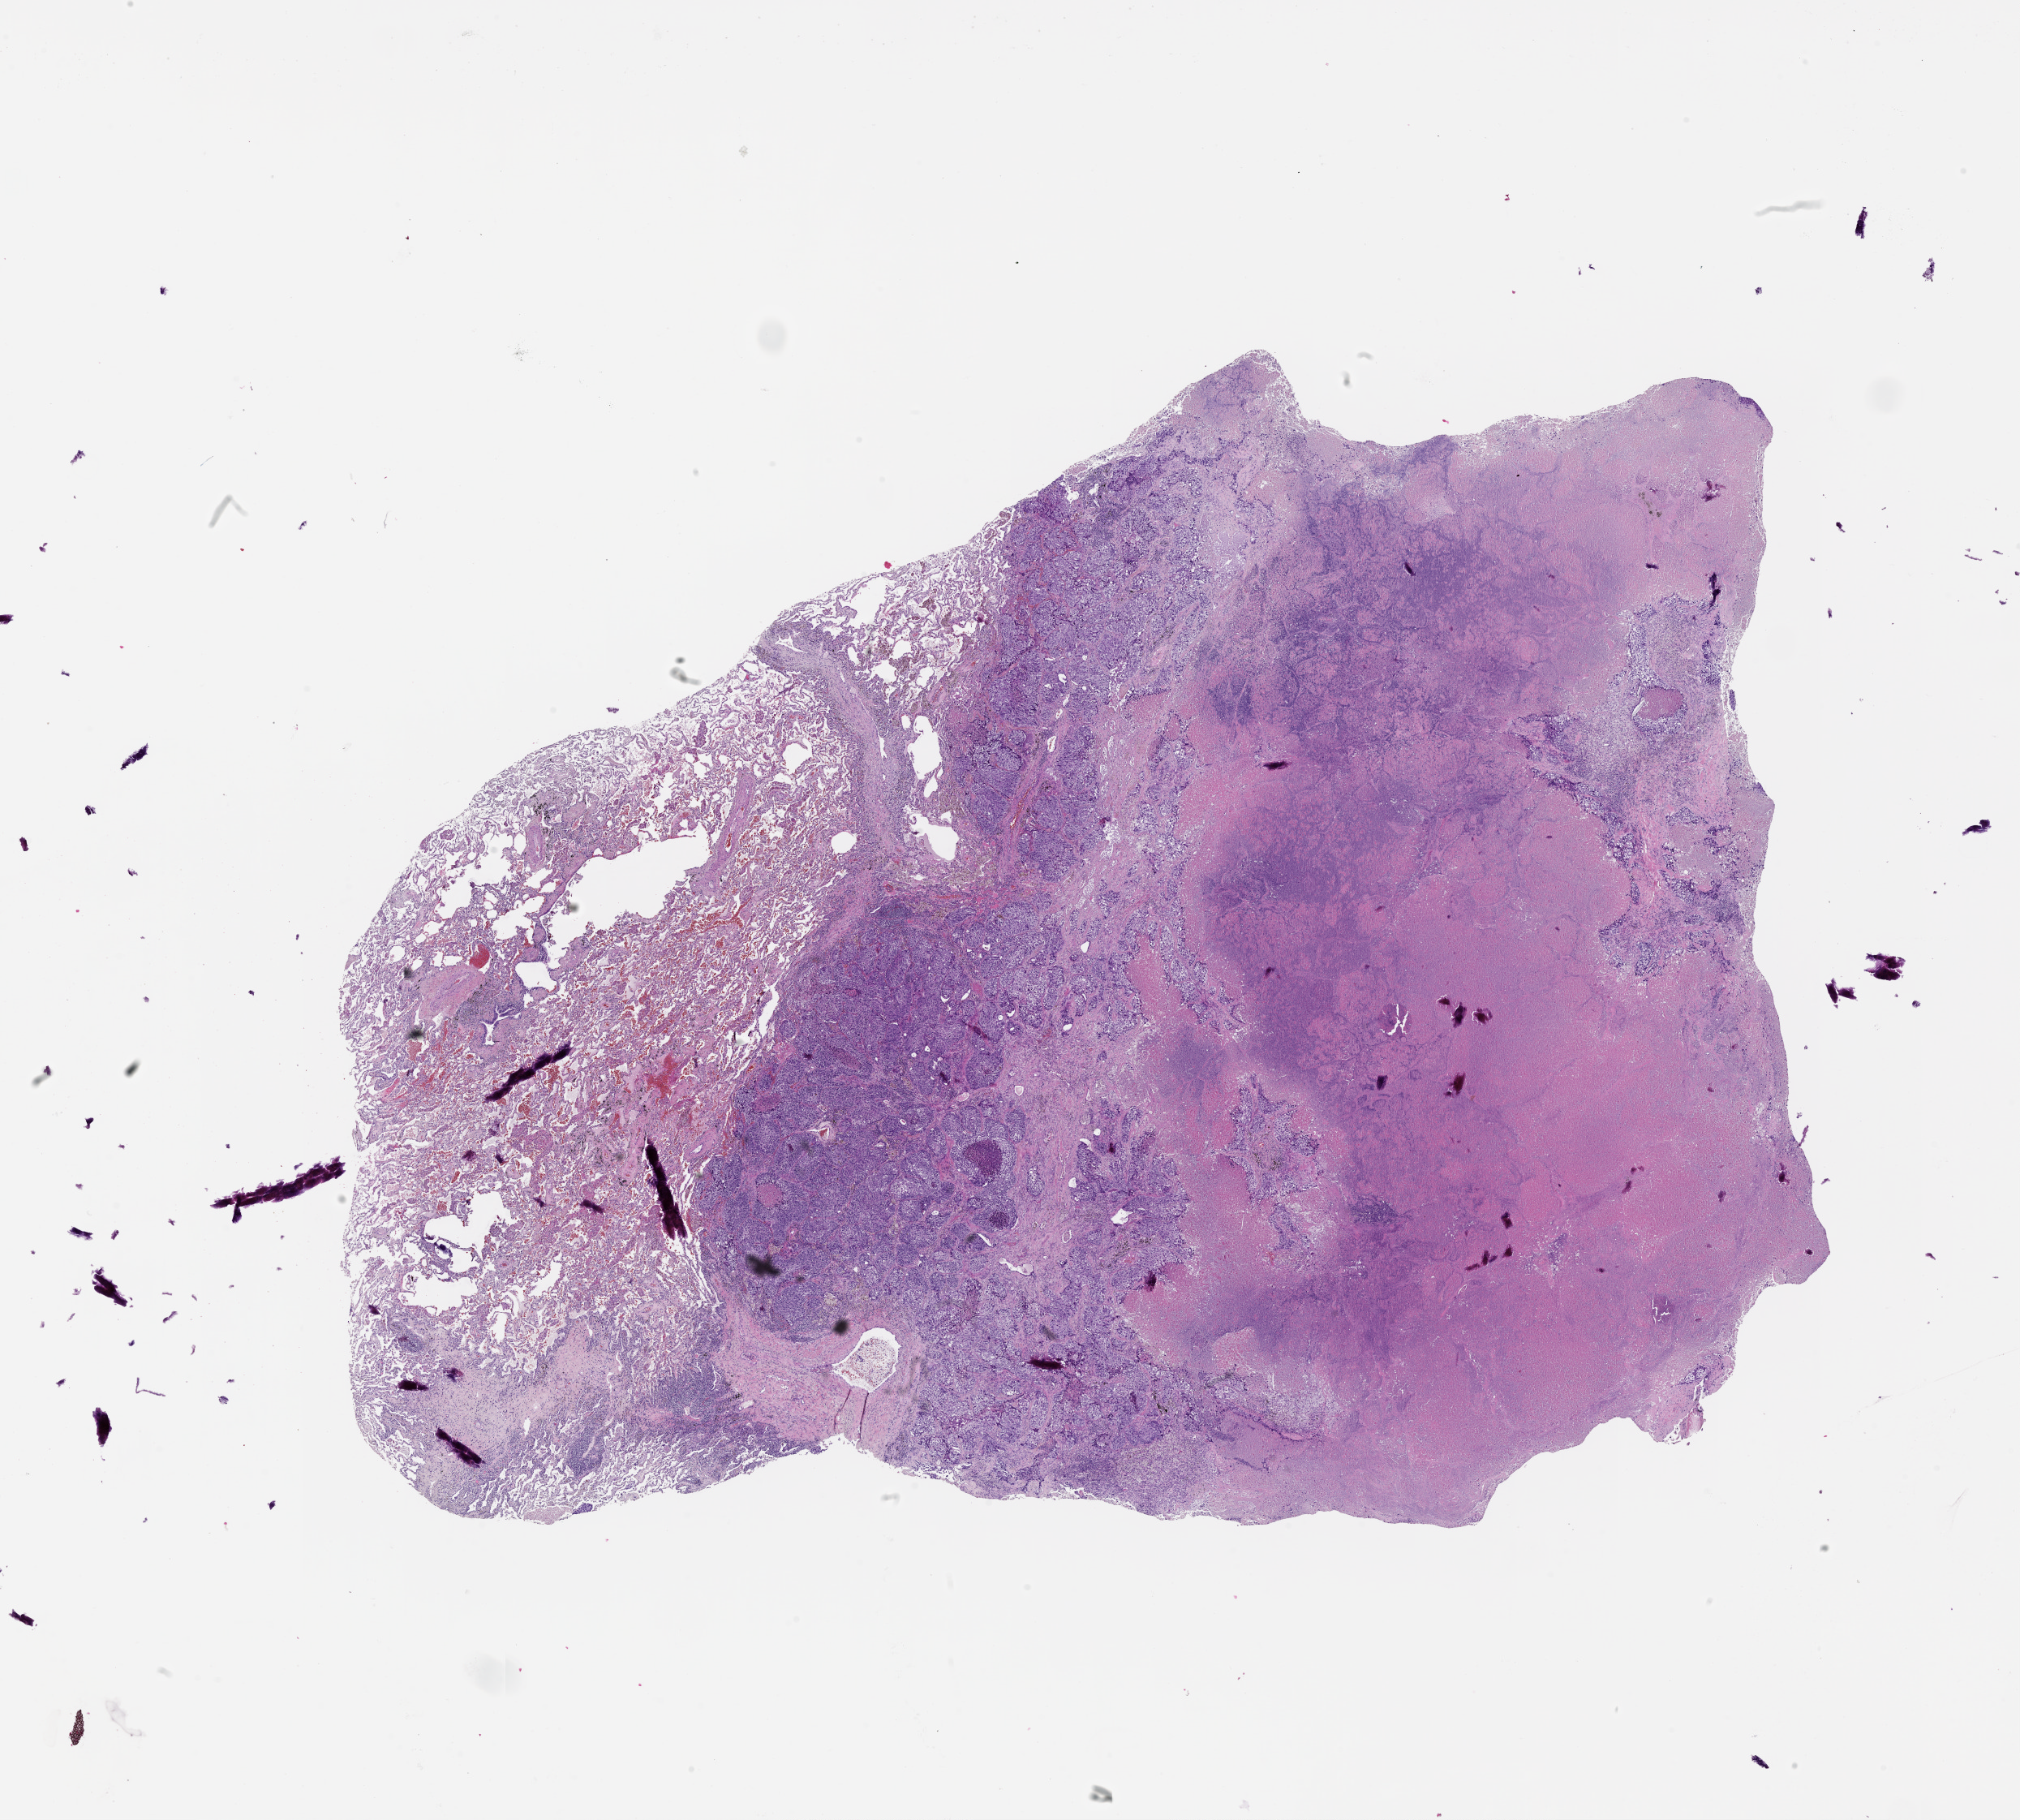
Hematoxylin and eosin (H&E) stained whole-slide image, a low-resolution overview of the entire scanned area, about 20.0 x 18.1 mm; tumour tissue sample, lung. 54-year-old male patient.
Patient diagnosis (cohort enrolment): squamous cell carcinoma (lung).